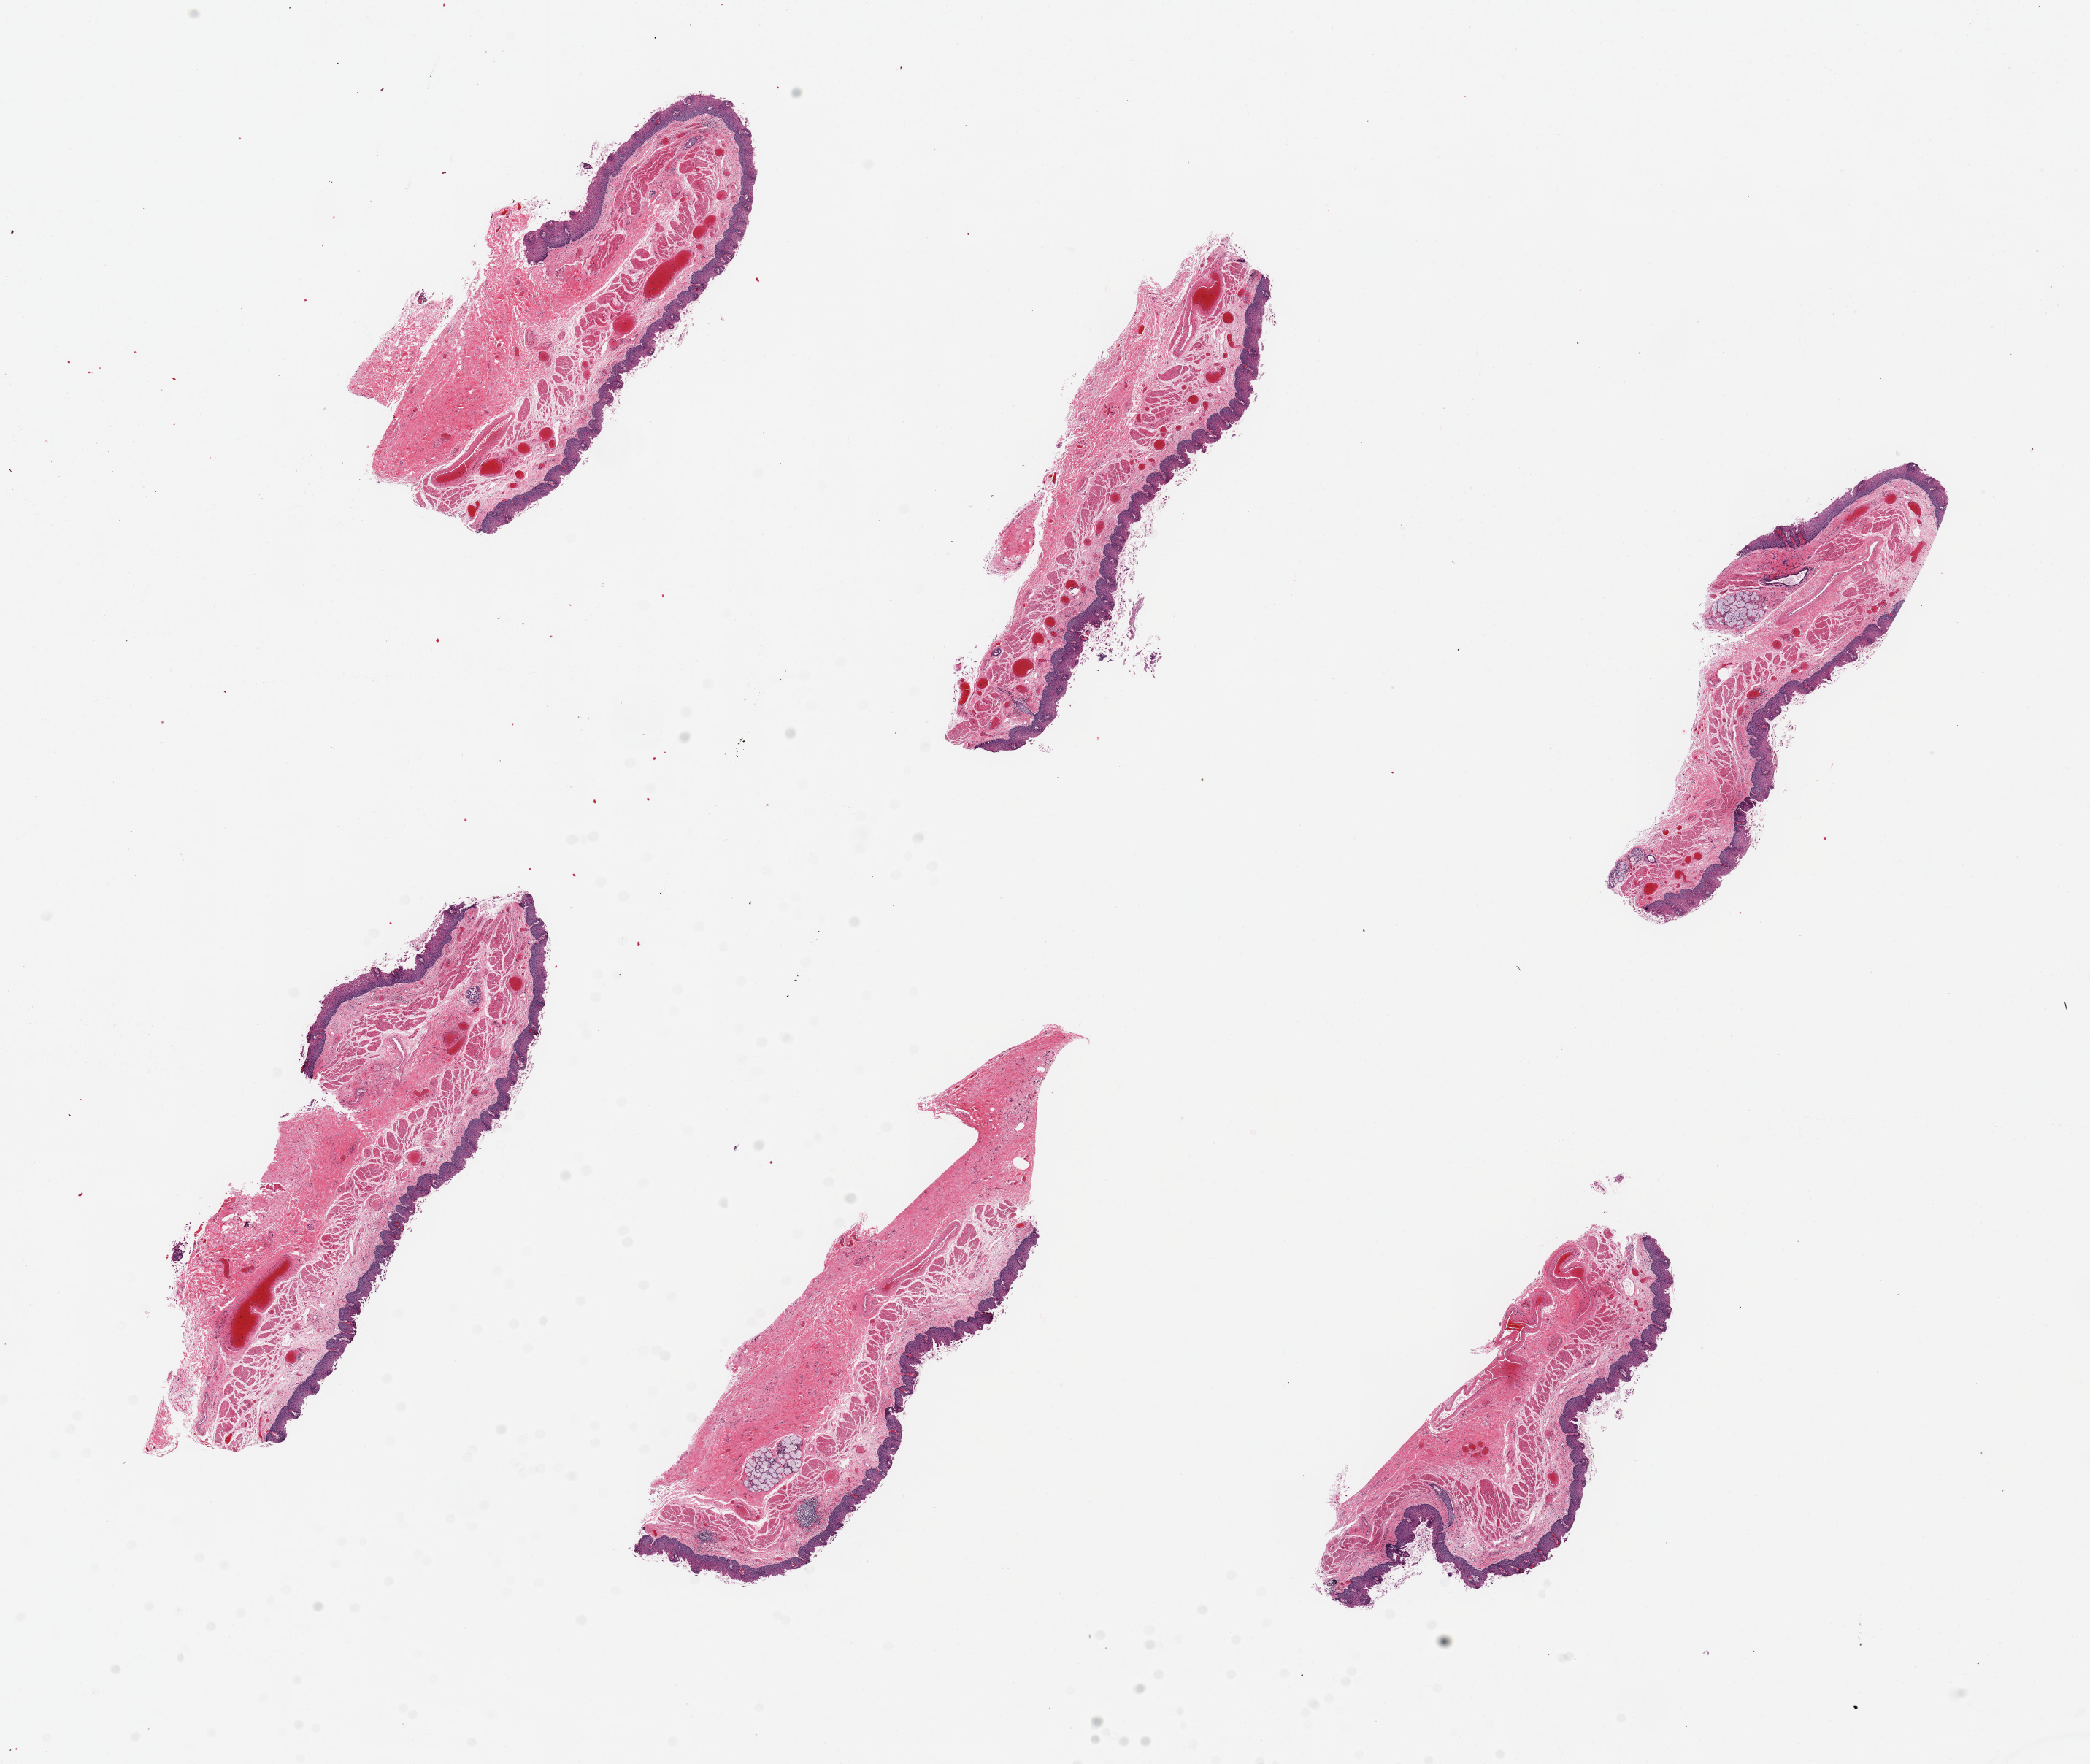
Whole-slide image, hematoxylin and eosin (H&E) stain — whole scanned area (about 22.6 x 19.1 mm) shown as a low-resolution overview. PAXgene-fixed, paraffin-embedded tissue. Sampled site (target tissue): esophageal mucous membrane. Donor tissue sample.
Pathologist's review note for this sample: 6 pieces, up to 7x2mm; Superficial sloughing.